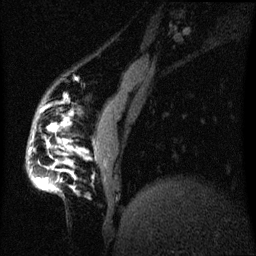
Breast MRI (dynamic contrast-enhanced), one sagittal slice. Dynamic contrast-enhanced series, image 2 of 3 at this slice position (ordered by acquisition). 1.5 T. TE 4.2 ms, TR 8 ms. 2.2 mm slice thickness. 256 × 256 image matrix, field of view 200 × 200 mm. Patient: female, 50 years.
Outlined on this slice (semi-automatically segmented with operator editing):
- analysis volume of interest (the breast-tissue region the enhancement analysis was run in; not a lesion): bounding box (x1, y1, x2, y2) in pixels: (25, 134, 67, 193)
- tumour enhancement mask (voxels above the 70 % enhancement threshold inside the analysis volume of interest): (38, 182, 44, 187)